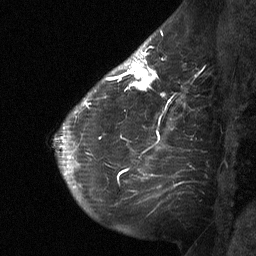
Breast MRI (dynamic contrast-enhanced), one sagittal slice. Position 43 of 64 along the scan axis. Dynamic contrast-enhanced study with each time point stored as its own series, time point 2 of 3 at this slice position (early post-contrast, ordered by acquisition time). 1.5 T. TE 4.8 ms, TR 27 ms. 2 mm slice thickness. 256 × 256 image matrix. Female patient, age 51 years. Case-level facts recorded for this patient, not image findings: setting: breast cancer imaged before/during neoadjuvant chemotherapy; receptor status: HR-positive, HER2-negative.
Outlined on this slice (semi-automatically segmented with operator editing):
- analysis volume of interest (the breast-tissue region the enhancement analysis was run in; not a lesion): bounding box (x1, y1, x2, y2) in pixels: (112, 46, 168, 106)
- tumour enhancement mask (voxels above the 90 % enhancement threshold inside the analysis volume of interest): (112, 46, 158, 91)